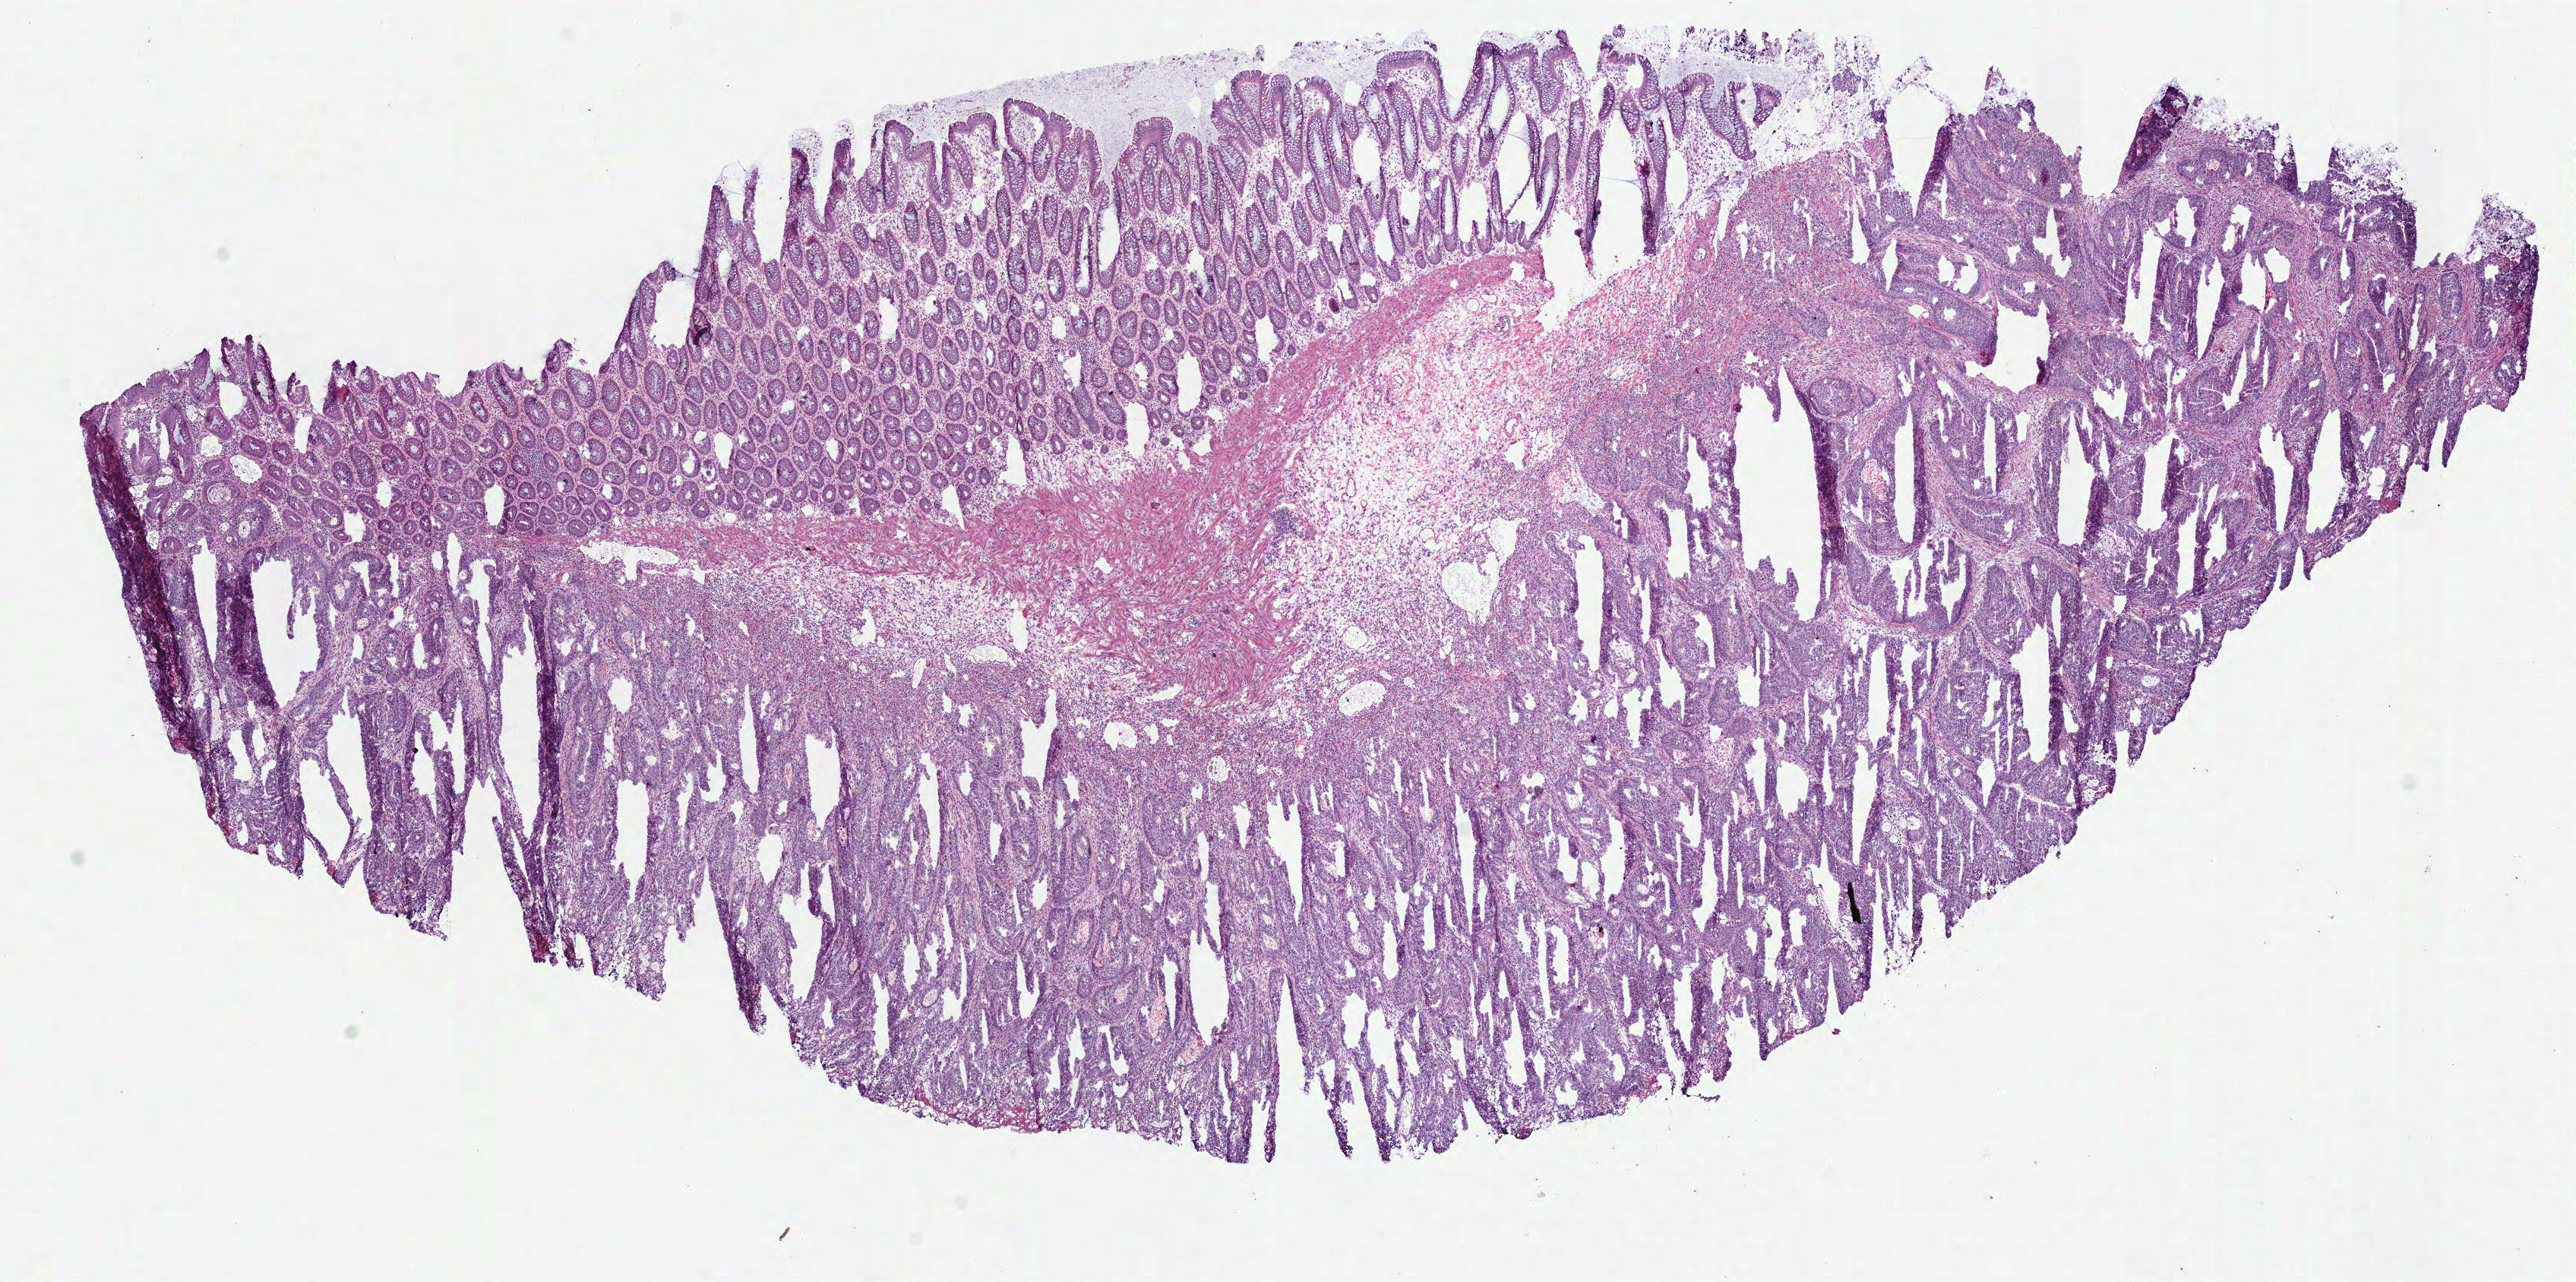
Hematoxylin and eosin (H&E) stained whole-slide image — a low-resolution overview of the entire scanned area, about 13.4 x 6.7 mm. Frozen section from the bottom of the tissue portion. Colon, primary tumour sample. Female, age 76 years at initial diagnosis. Composition of this section per pathologist review: tumour cells 58%, tumour nuclei 60%, normal cells 32%, stromal cells 10%, necrosis 0%. Inflammatory infiltration, as recorded: lymphocyte infiltration 3%, monocyte infiltration 0%, neutrophil infiltration 0%.
Lymph nodes positive (case pathology): 0 of 5 examined. Histologic diagnosis: Adenocarcinoma, NOS (sigmoid colon). AJCC pathologic stage: IIA (7th edition).